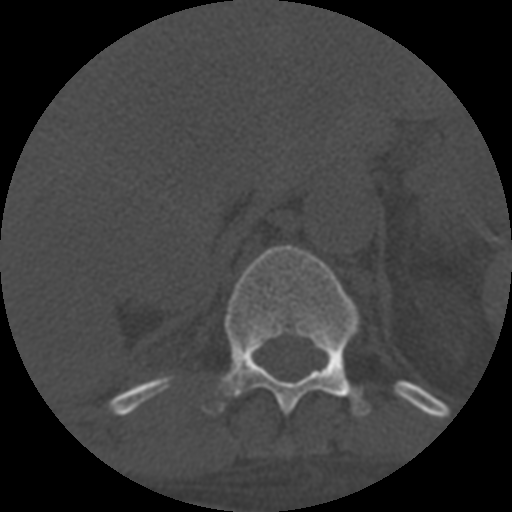
CT including the spine, one axial slice; slice 336 of 708 in the series (ordered by position); reconstruction kernel STANDARD; one of 3 acquisitions stored at this slice position; bone window (W 1800 / L 400 HU); 512 × 512 image matrix, field of view 160 × 160 mm. Patient age 55 years. From the clinical record (not read from this slice): primary cancer: colon; vertebrae with lytic lesions (as recorded): T12, L1, L5.
Structures marked on this image (semi-automatically segmented with operator editing):
- T11 vertebra: box from (x=204, y=245) to (x=370, y=417) px